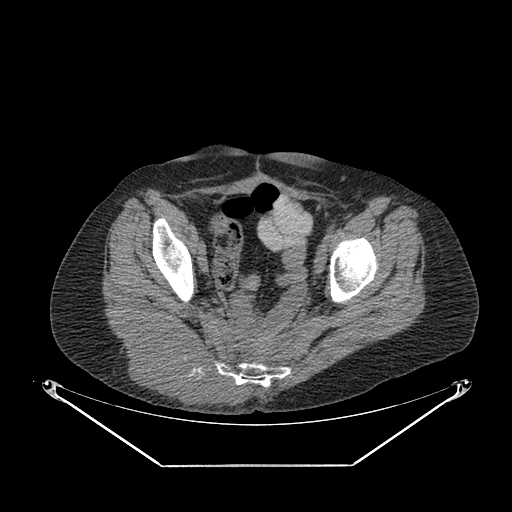
CT of an extremity soft-tissue mass (from a PET/CT study), one axial slice; position 63 of 267 along the scan axis; soft-tissue window (W 400 / L 40 HU); 3.75 mm slice thickness; 512 × 512 image matrix. Female patient. Case-level facts recorded for this patient, not image findings: histological type: spindle cell suggestive of myxofibrosarcoma; grade: intermediate; site of the primary tumour: right buttock.
Structures marked on this image (expert contour drawn on MRI and transferred to this co-registered scan by the dataset authors):
- gross tumour volume (mass): box from (x=119, y=320) to (x=243, y=407) px